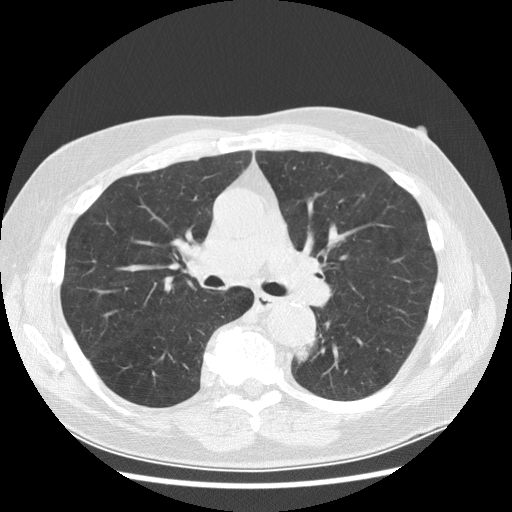
Low-dose screening chest CT, axial slice; first (baseline) screen; lung window (W 1500 / L -600 HU); 2.5 mm slice thickness; standard (soft-tissue) reconstruction kernel (STANDARD); 512 × 512 image matrix, field of view 370 × 370 mm. Male, age 70 years at enrolment. Current smoker at enrolment.
• Expert-annotated lung lesion, box from (x=278, y=324) to (x=332, y=385) px.
• Reader record for this screening exam (exam-level; its link to the box is not recorded): non-calcified nodule or mass ≥4 mm, left lower lobe, 27 × 16 mm, spiculated (stellate) margins, soft tissue attenuation, pre-existing on the prior screen: yes; interval growth: yes.
• Lung cancer was diagnosed 97 days after this screen: papillary adenocarcinoma, NOS, left lower lobe, moderately differentiated (G2), stage IB (AJCC 6th edition), 35 mm at pathology.